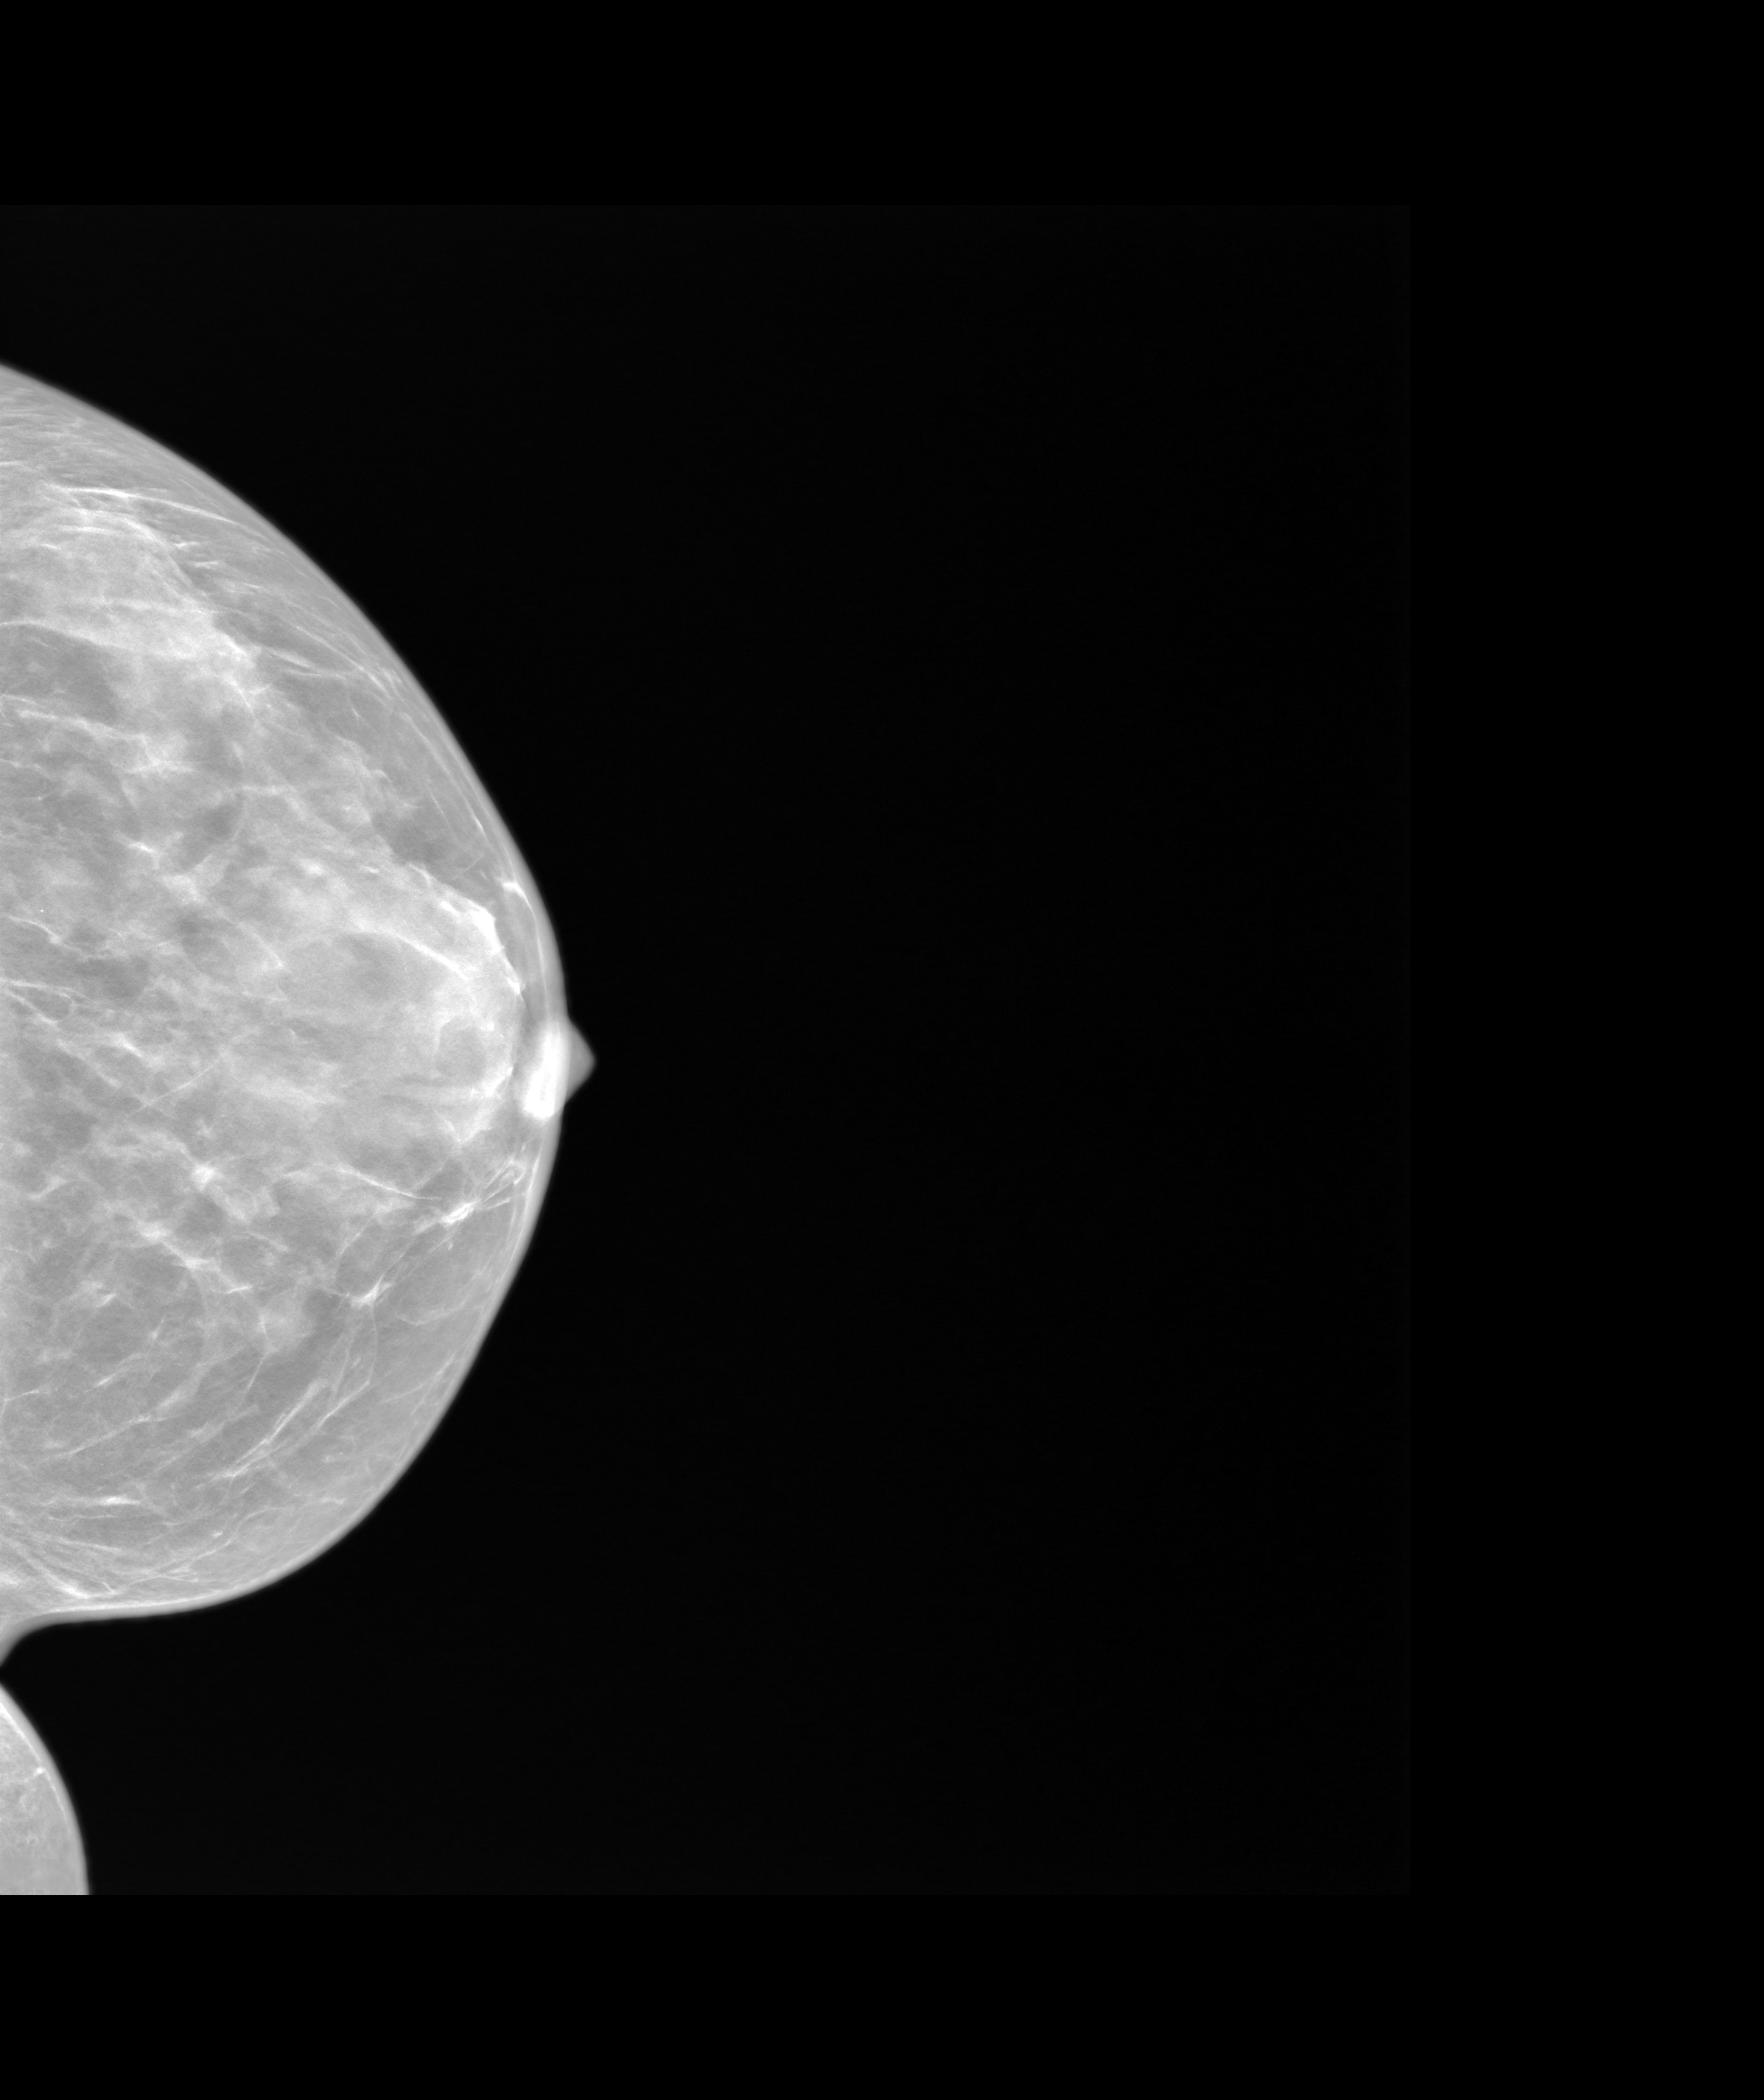
Annual screening mammography examination. Patient: female, 49 years.
Image type: synthesized 2-D view from tomosynthesis. Breast: left. Projection: CC view.